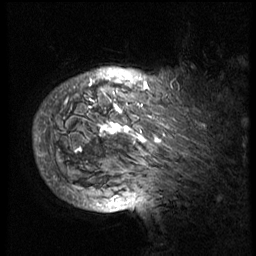
Breast MRI (dynamic contrast-enhanced), one sagittal slice. Slice 61 of 74 in the series (ordered by position). 3 images stored at this slice position (order not interpretable as contrast timing). 1.5 T. TE 4.2 ms, TR 8.9 ms. 256 × 256 image matrix, field of view 200 × 200 mm. Patient: female, 57 years. Case-level facts recorded for this patient, not image findings: setting: breast cancer imaged before/during neoadjuvant chemotherapy; receptor status: HER2-positive.
Annotated regions visible in this slice (semi-automatic segmentation, software-assisted and operator-edited):
- analysis volume of interest (the breast-tissue region the enhancement analysis was run in; not a lesion): bounding box [x1, y1, x2, y2] px = [40, 62, 242, 175]
- tumour enhancement mask (voxels above the 140 % enhancement threshold inside the analysis volume of interest): [40, 77, 162, 161]